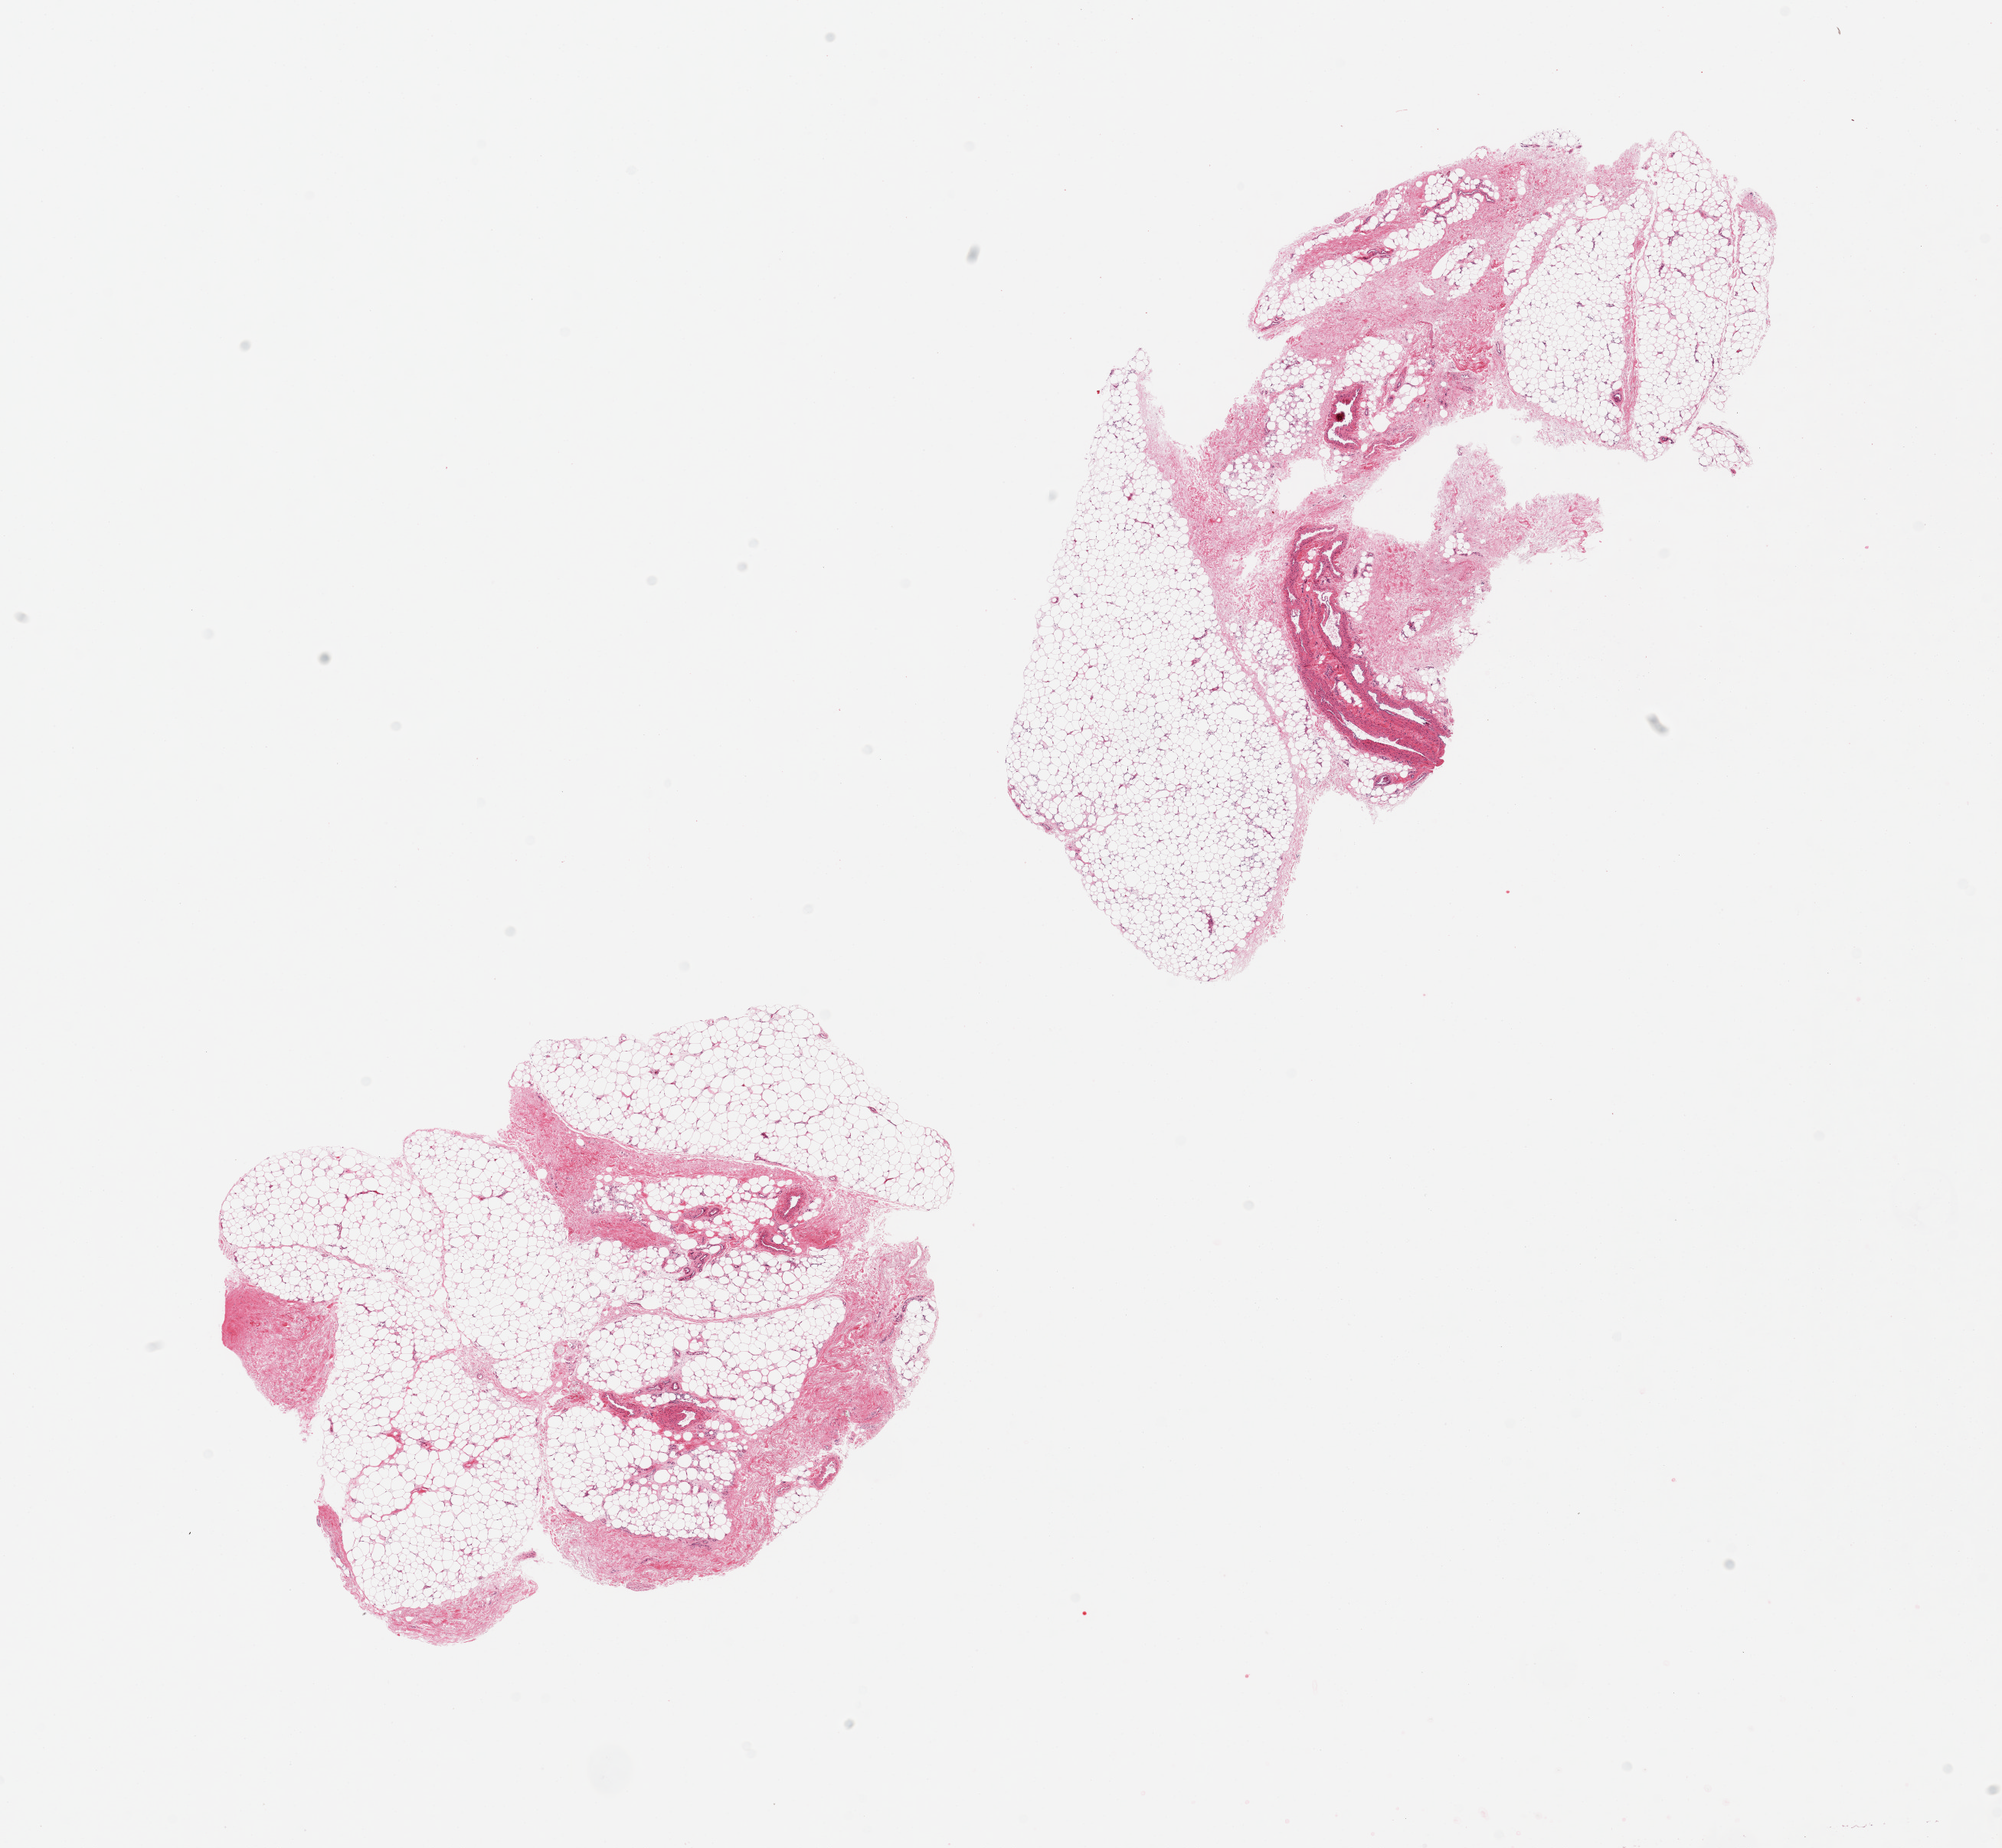
Whole-slide image, haematoxylin and eosin stain, whole scanned area (about 20.7 x 19.1 mm, from a 20x scan) shown as a low-resolution overview; PAXgene-fixed, paraffin-embedded tissue; section of adipose tissue (target tissue); tissue donor sample.
Pathologist's review note for this sample: 2 pieces; fat with 10 and 20% fibrous tissue and vessels.